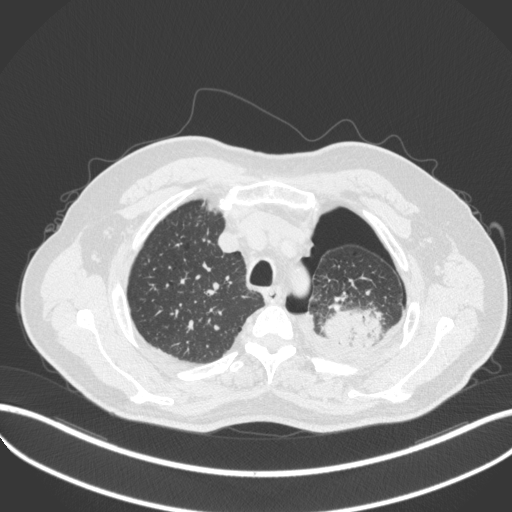
Chest CT, one axial slice; position 410 of 466 along the scan axis; 120 kVp; lung window (W 1500 / L -600 HU); 1 mm slice thickness; 512 × 512 image matrix. Male patient, age 76 years. Case-level facts recorded for this patient, not image findings: clinical TNM (as recorded): T3 N0 M1b.
Structures marked on this image (rectangle marked by the reading radiologist):
- lung tumour (recorded histology: adenocarcinoma): bounding box <320,308,390,351> (left, top, right, bottom; pixels)